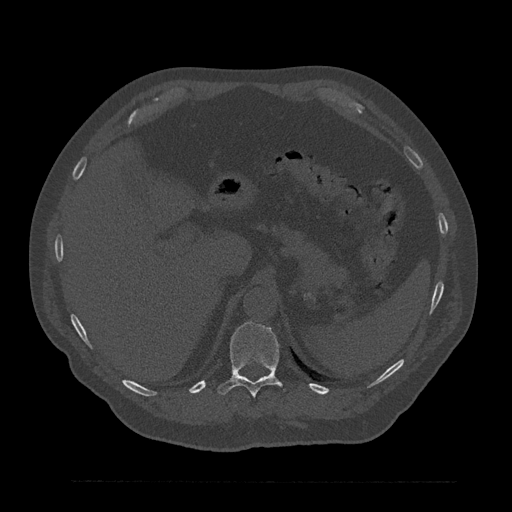
CT including the spine, one axial slice; slice 291 of 797 in the series (ordered by position); bone window (W 1800 / L 400 HU); 512 × 512 image matrix, field of view 430 × 430 mm. Patient: male, 61 years. Case-level facts recorded for this patient, not image findings: primary cancer: prostate.
Structures marked on this image (semi-automatically segmented with operator editing):
- T11 vertebra: bounding box [x1, y1, x2, y2] px = [217, 322, 283, 397]